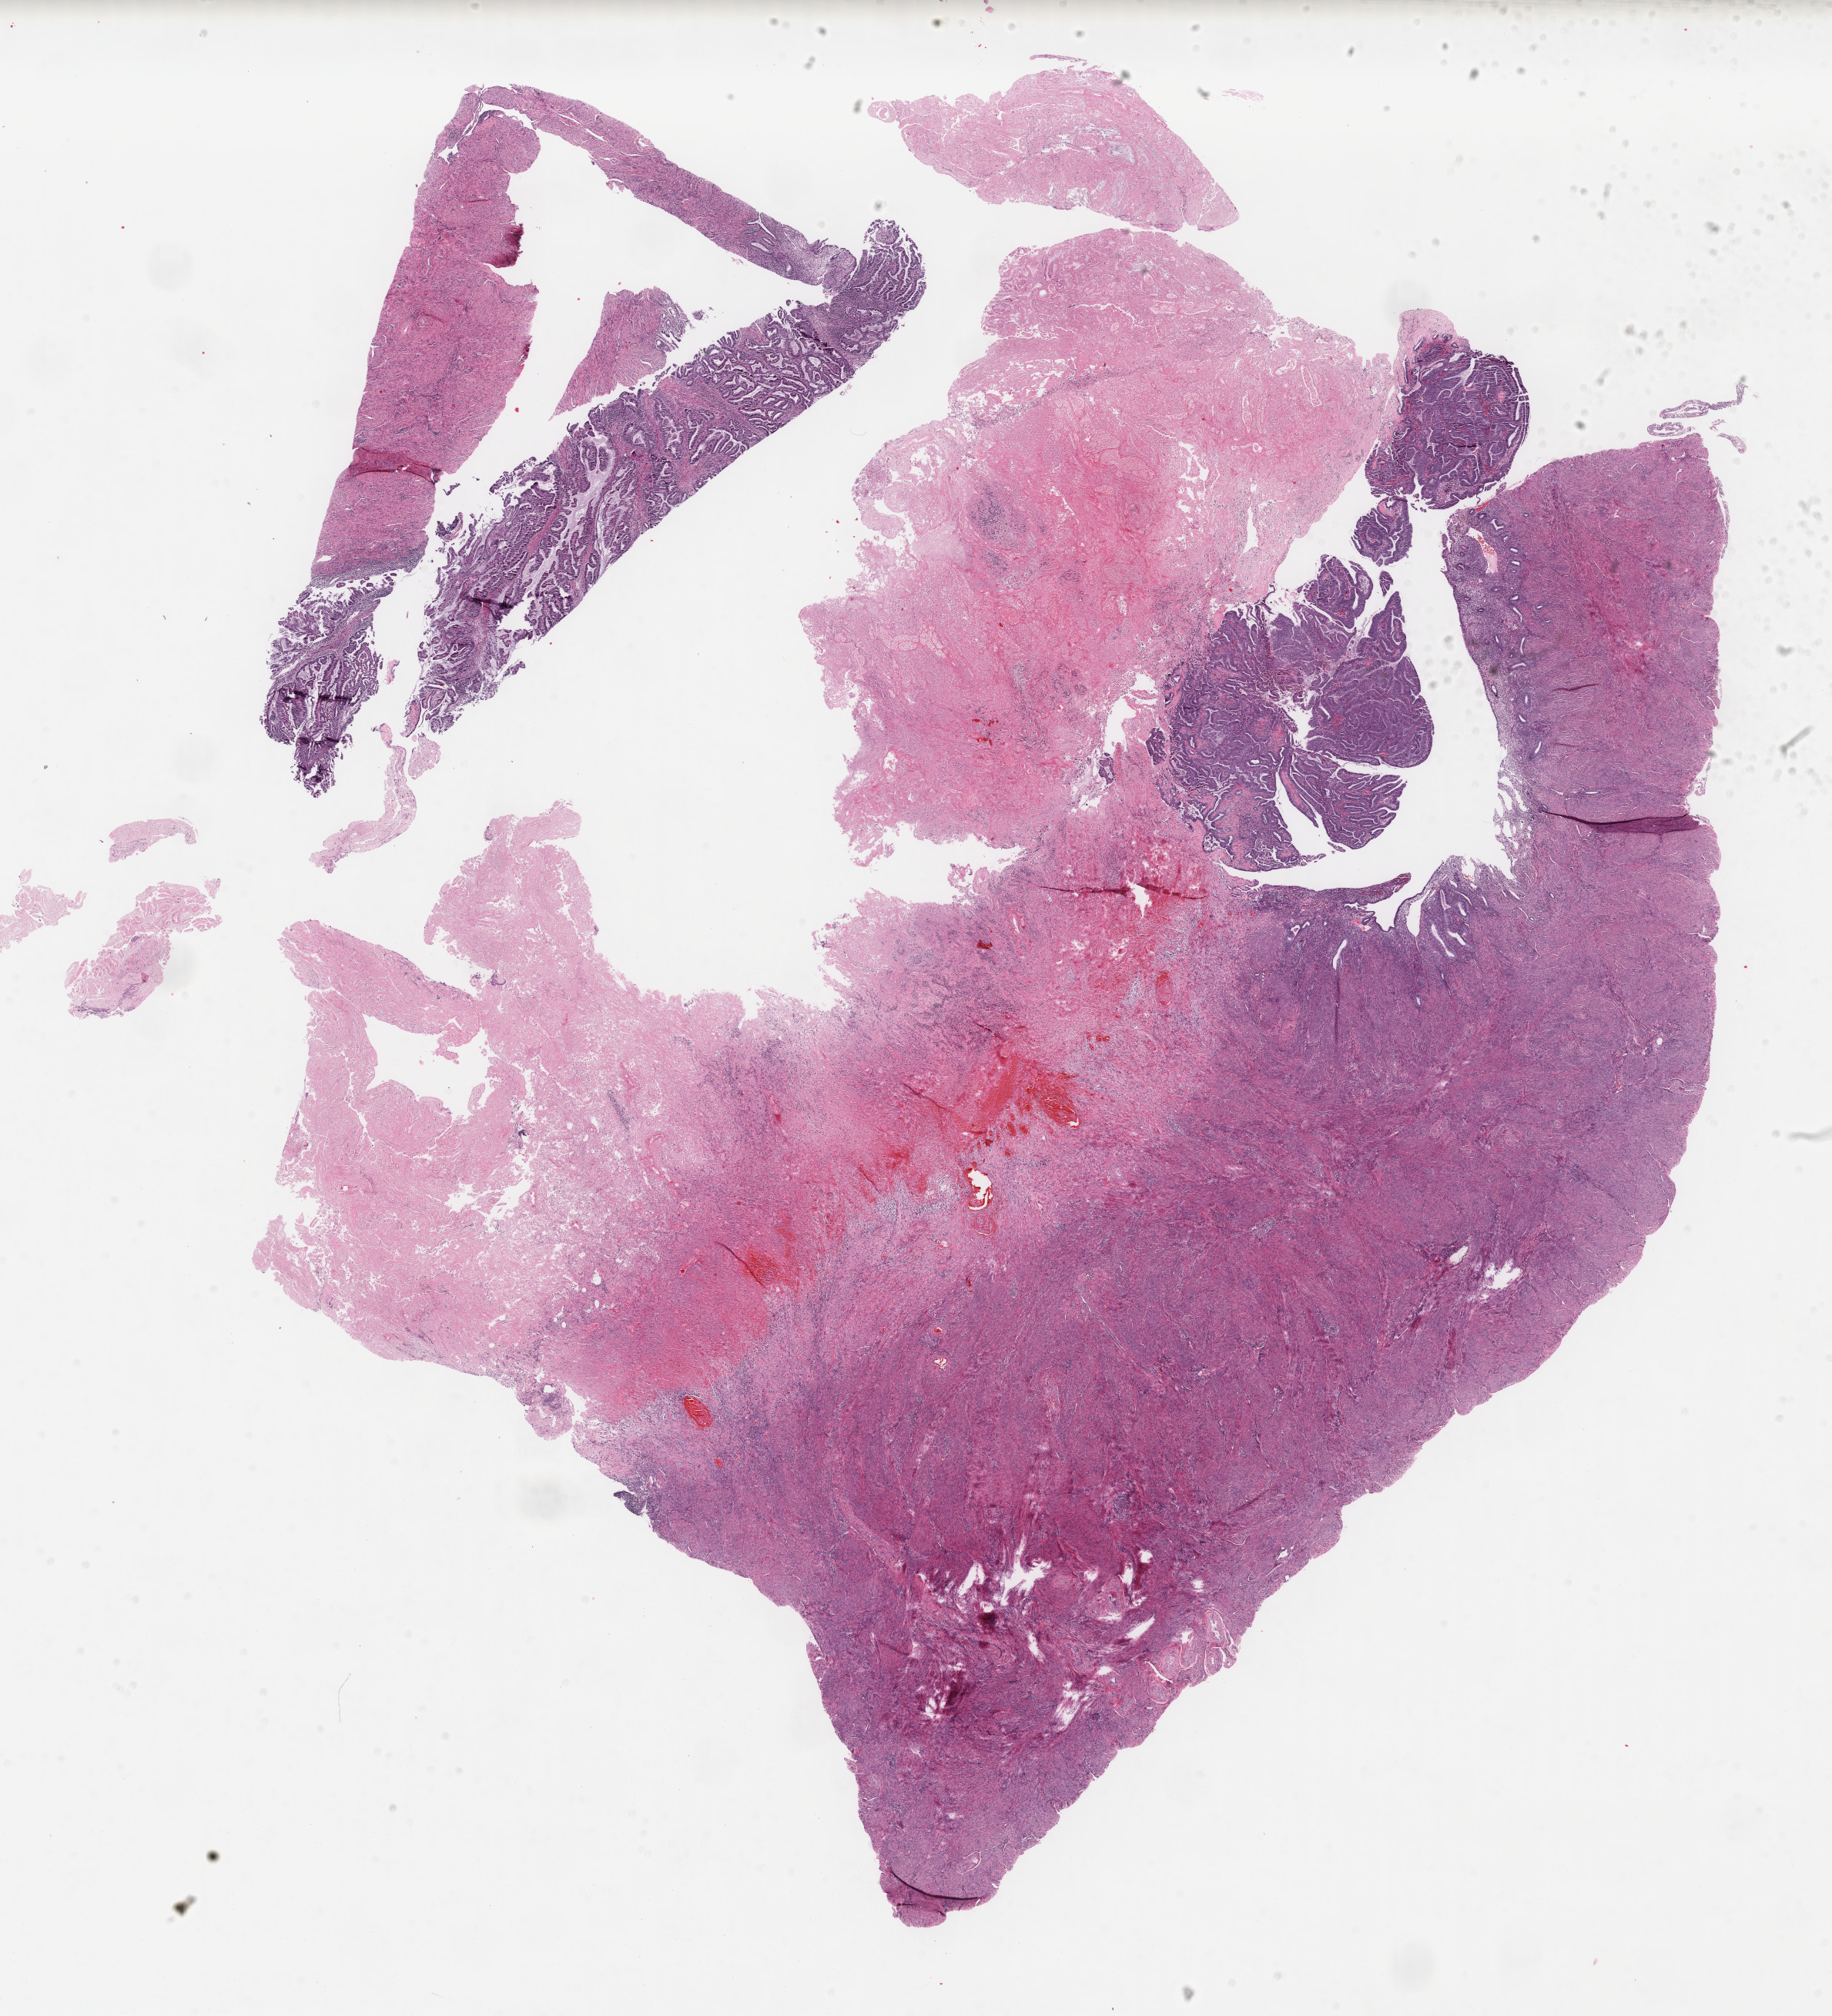
Digitized H&E-stained tissue section (whole slide), whole scanned area (about 18.9 x 20.8 mm, from a 40x scan) shown as a low-resolution overview, formalin-fixed paraffin-embedded (FFPE) diagnostic section, primary tumour sample from the uterus. Patient: female, age at initial diagnosis 50 years. Histologic grade: G2 (moderately differentiated).
* FIGO stage: IIIC
* histologic diagnosis: Endometrioid adenocarcinoma, NOS